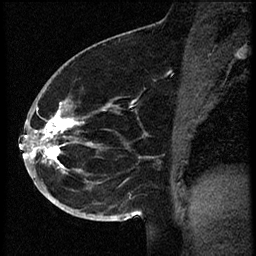
Breast MRI (dynamic contrast-enhanced), one sagittal slice; dynamic contrast-enhanced study with each time point stored as its own series, time point 2 of 3 at this slice position (early post-contrast, ordered by acquisition time); 1.5 T; TE 4.2 ms, TR 18.9 ms; 2 mm slice thickness; 256 × 256 image matrix. Female patient. Case-level facts recorded for this patient, not image findings: setting: breast cancer imaged before/during neoadjuvant chemotherapy; receptor status: HR-positive, HER2-negative.
Structures marked on this image (semi-automatic segmentation, software-assisted and operator-edited):
- analysis volume of interest (the breast-tissue region the enhancement analysis was run in; not a lesion): box from (x=30, y=87) to (x=114, y=173) px
- tumour enhancement mask (voxels above the 100 % enhancement threshold inside the analysis volume of interest): (x=30, y=103)–(x=82, y=168)